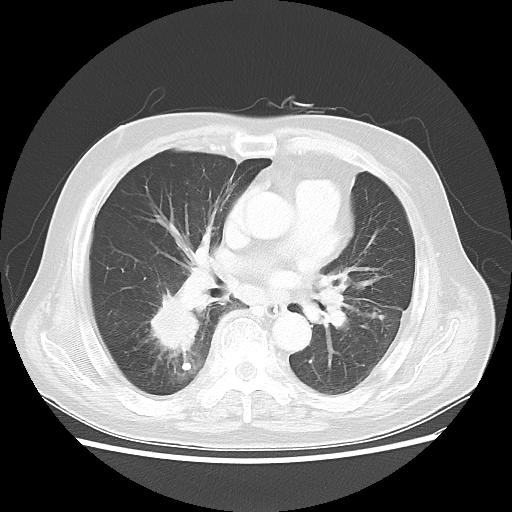
Chest CT, one axial slice; position 19 of 44 along the scan axis; lung window (W 1500 / L -600 HU); 512 × 512 image matrix, field of view 359 × 359 mm. Patient: male, 83 years. From the clinical record (not read from this slice): clinical TNM (as recorded): T2 N3 M0.
Annotated regions visible in this slice (rectangle marked by the reading radiologist):
- lung tumour (recorded histology: adenocarcinoma): bounding box [x1, y1, x2, y2] px = [147, 290, 203, 353]